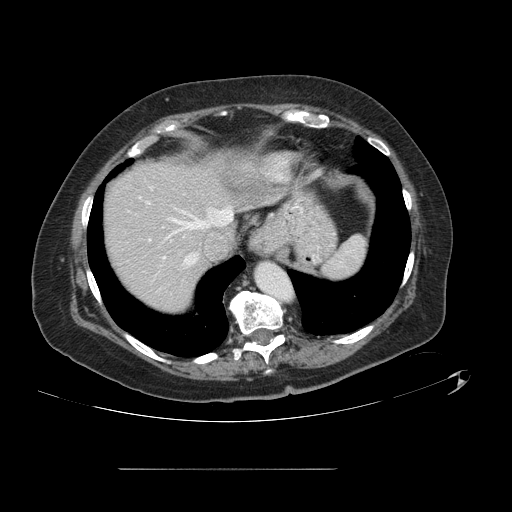
Contrast-enhanced abdominal CT, one axial slice; position 113 of 148 along the scan axis; intravenous contrast given; soft-tissue window (W 400 / L 40 HU); 2.5 mm slice thickness; 512 × 512 image matrix, field of view 439 × 439 mm. Female patient, age 75 years. Case-level facts recorded for this patient, not image findings: diagnosis: colorectal cancer liver metastases, imaged before liver resection; multiple liver metastases: no; largest metastasis: 2.4 cm.
Outlined on this slice (expert manual segmentation):
- hepatic veins: bounding box <172,206,233,266> (left, top, right, bottom; pixels)
- liver: <104,156,250,312>
- planned liver remnant (the part of the liver to remain after resection): <104,154,257,312>